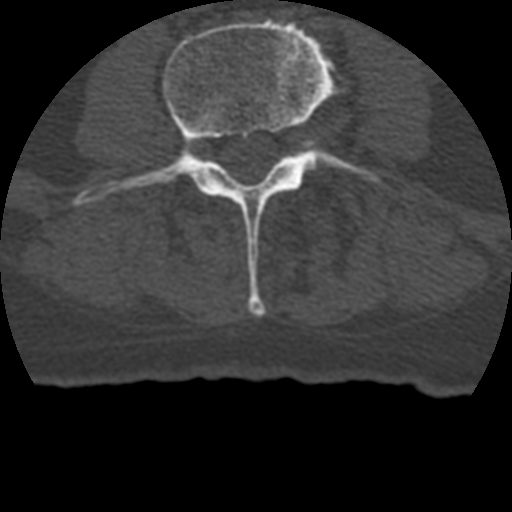
CT including the spine, one axial slice. 120 kVp. Bone window (W 1800 / L 400 HU). 512 × 512 image matrix, field of view 160 × 160 mm. Patient age 69 years. From the clinical record (not read from this slice): primary cancer: prostate.
Outlined on this slice (semi-automatic segmentation, software-assisted and operator-edited):
- L3 vertebra: box from (x=78, y=19) to (x=340, y=316) px